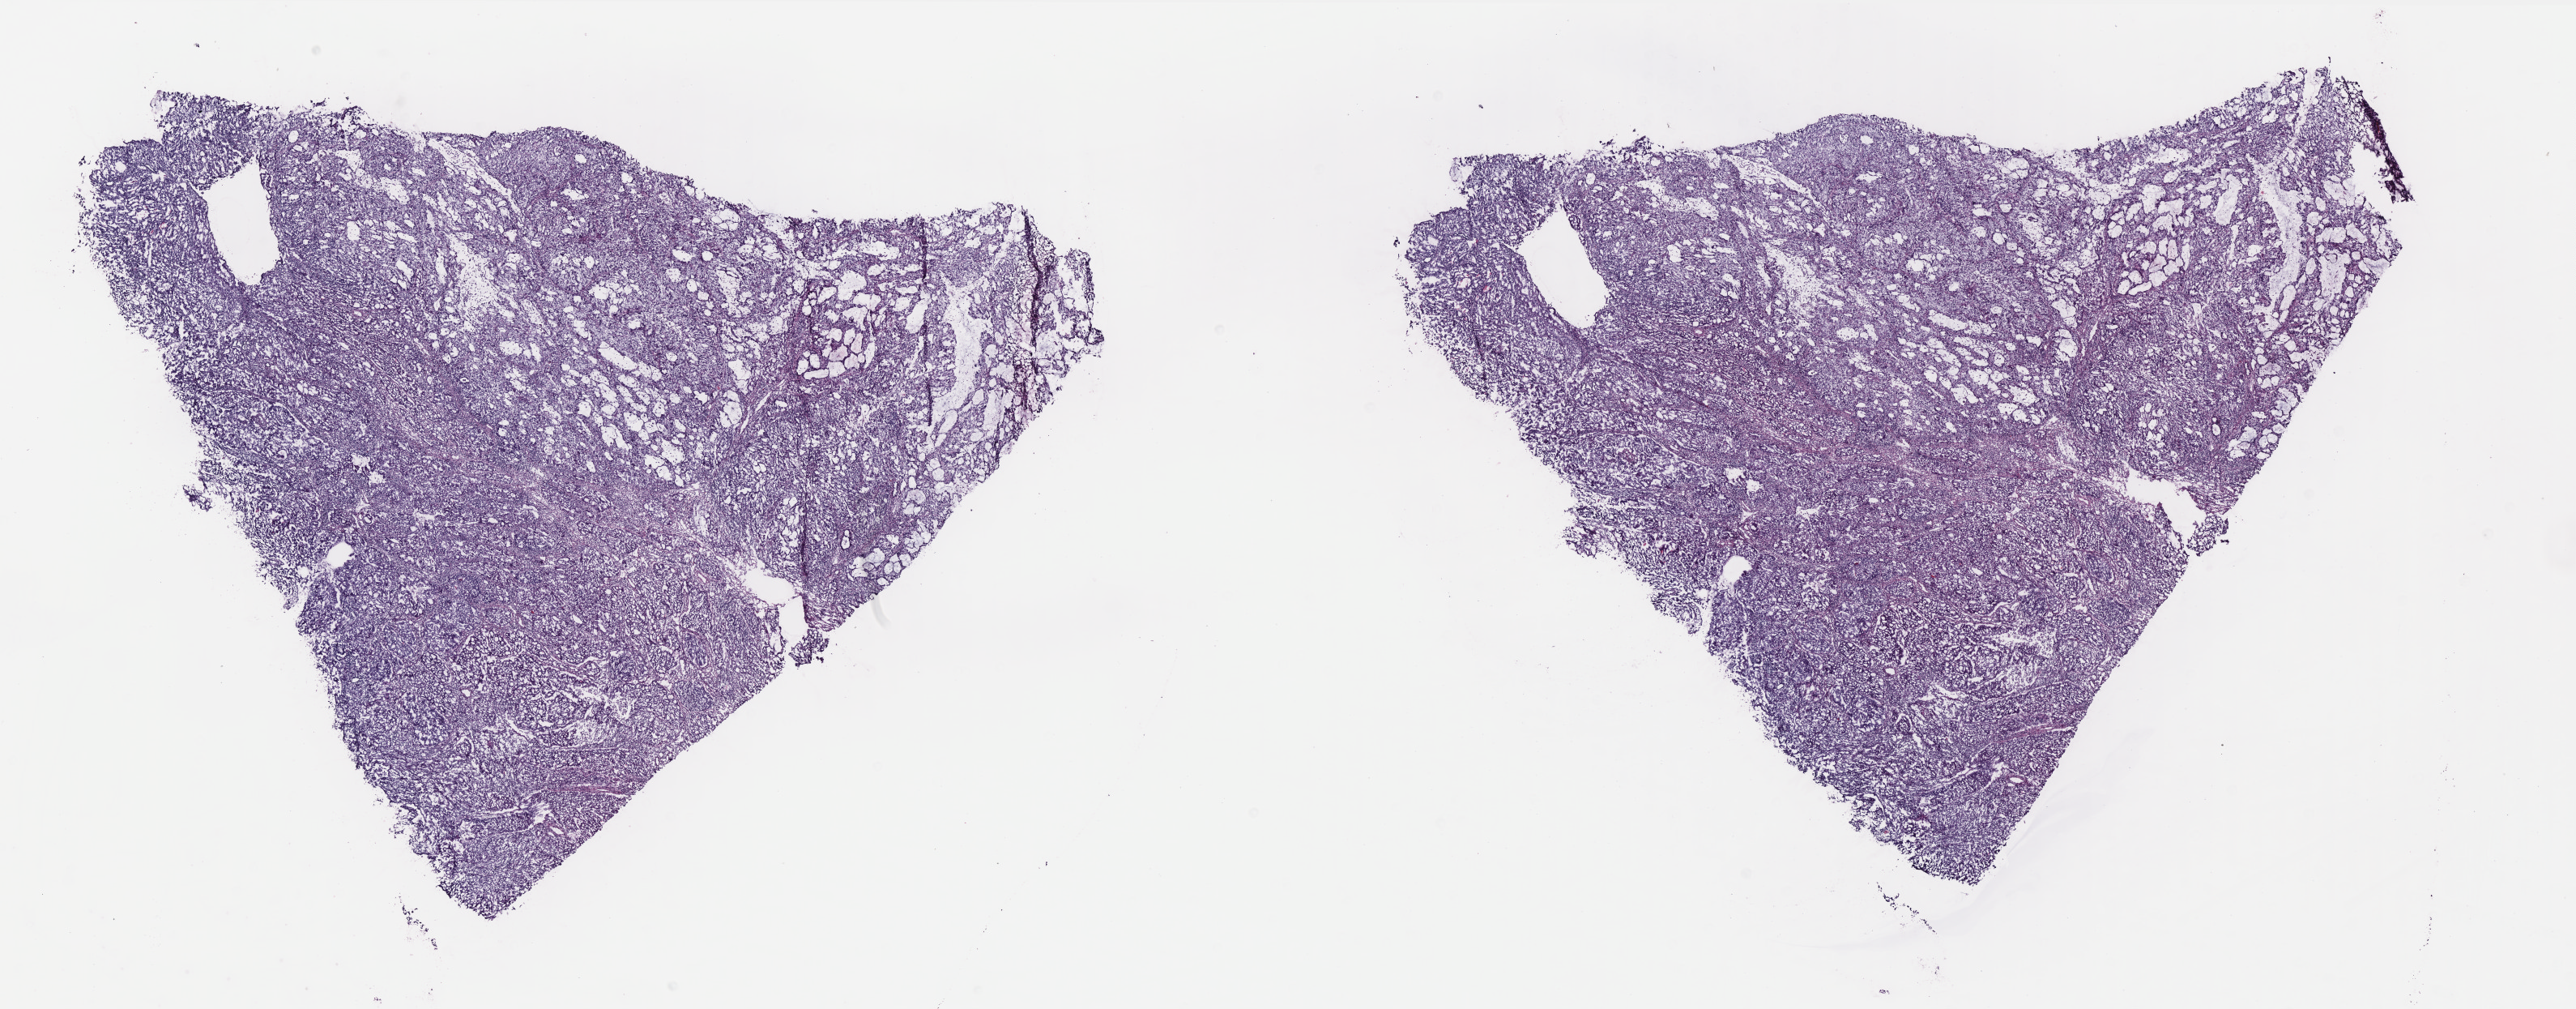
Whole-slide histology image, Hematoxylin and eosin (H&E) stained, whole scanned area (about 25.5 x 10.0 mm, slide scanned at 40x) shown as a low-resolution overview, frozen section from the top of the tissue portion, uterus, primary tumour sample. Patient: female, age at initial diagnosis 50 years. Pathologist review of this section (percent, as recorded): tumour cells 100%, tumour nuclei 90%.
Histologic diagnosis: Endometrioid adenocarcinoma, NOS (endometrium).